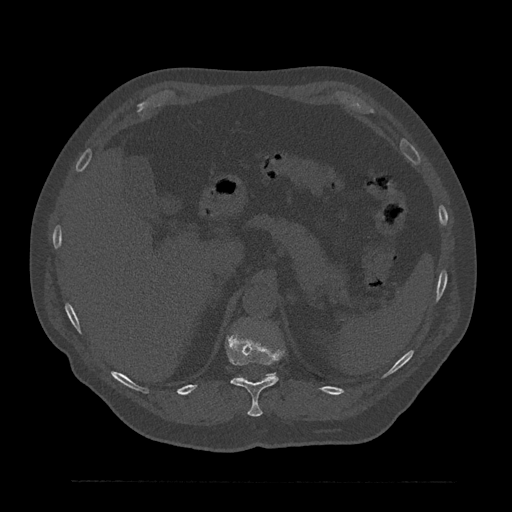
CT including the spine, one axial slice. Slice 277 of 797 in the series (ordered by position). Reconstruction kernel Br40s/3. 120 kVp. Bone window (W 1800 / L 400 HU). 0.5 mm slice thickness. 512 × 512 image matrix. Patient: male, 61 years. Case-level facts recorded for this patient, not image findings: primary cancer: prostate.
Structures marked on this image (semi-automatically segmented with operator editing):
- T11 vertebra: bounding box (x1, y1, x2, y2) in pixels: (226, 330, 283, 417)
- T12 vertebra: (270, 374, 273, 376)